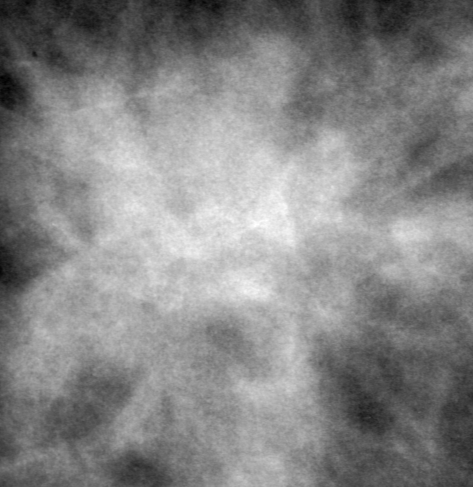
Cropped region of a digitized screen-film mammogram centred on a radiologist-marked abnormality, left breast, MLO view, BI-RADS breast density category 3 (scale 1–4).
- Mass, shape irregular, margins spiculated; BI-RADS assessment category 5; pathology result (as recorded, not read from the image): malignant.